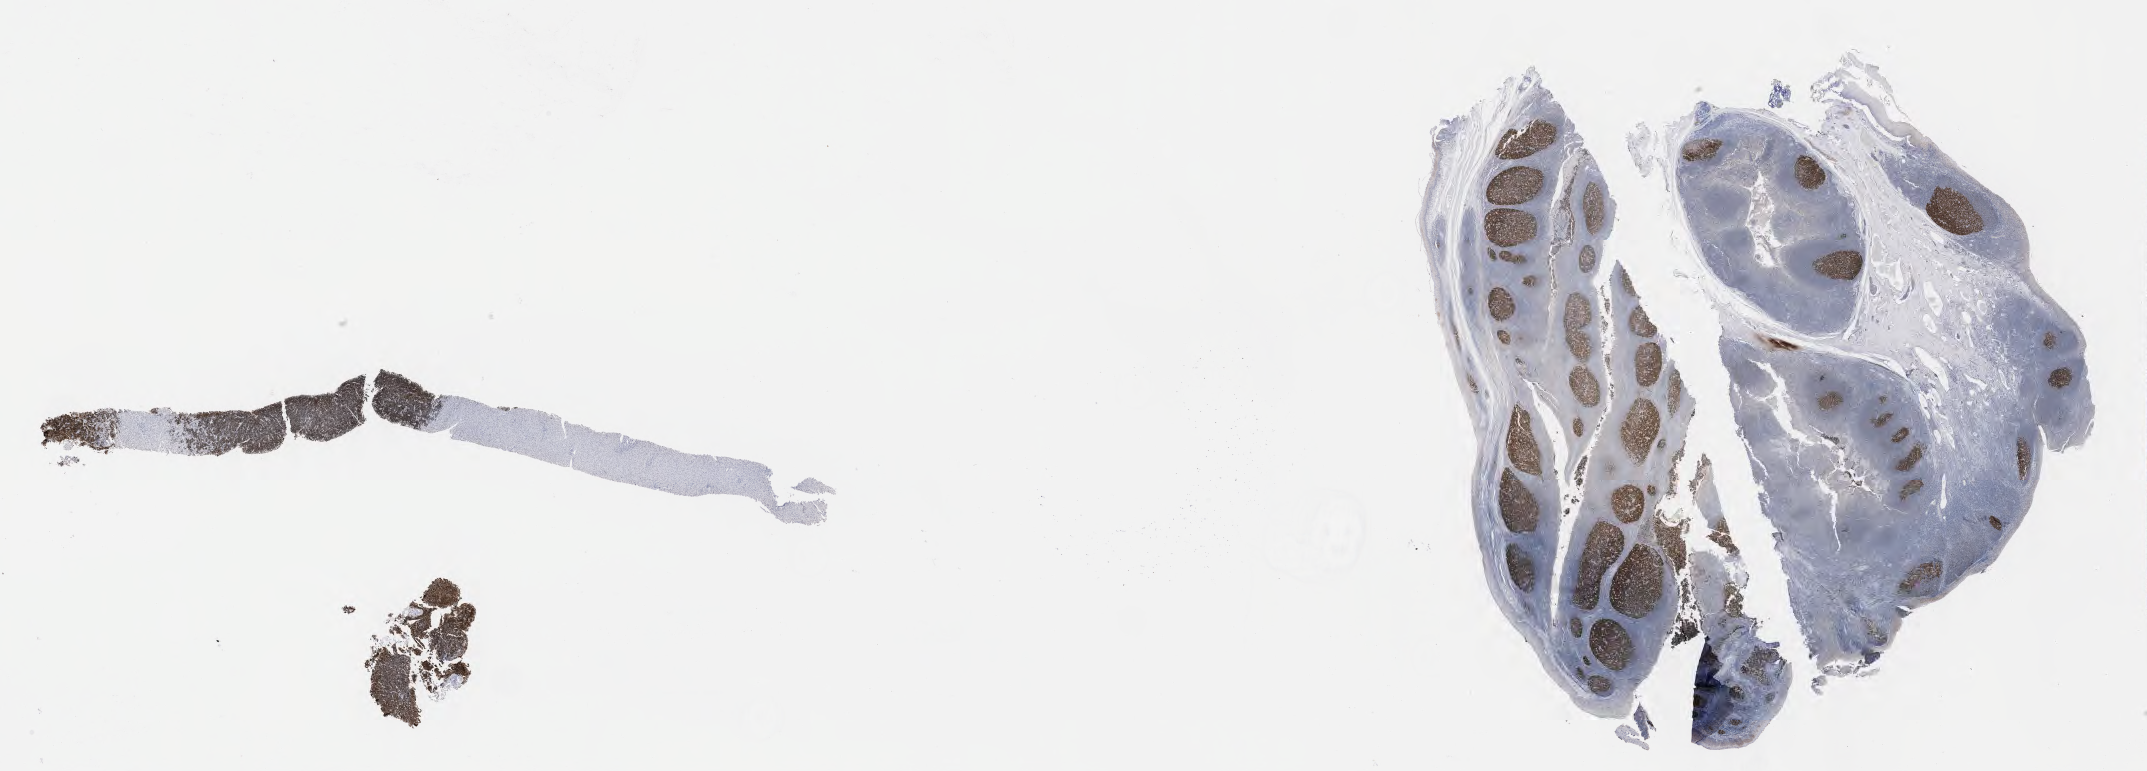
Immunohistochemistry (IHC) whole-slide image stained for BCL6, whole scanned area (about 34.7 x 12.5 mm) shown as a low-resolution overview; specimen: tumor tissue. Patient: male, aged 68.
• diagnosis: Burkitt lymphoma, NOS